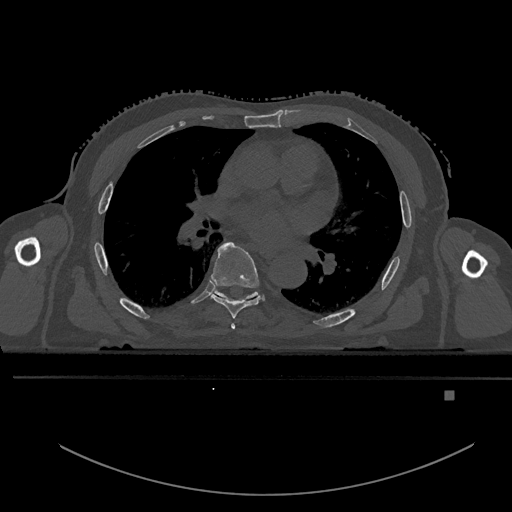
CT including the spine, one axial slice; position 296 of 969 along the scan axis; bone window (W 1800 / L 400 HU); 512 × 512 image matrix, field of view 456 × 456 mm. Male patient, age 82 years. From the clinical record (not read from this slice): primary cancer: prostate; vertebrae with lytic lesions (as recorded): T11, T9, T8, T2.
Structures marked on this image (semi-automatic segmentation, software-assisted and operator-edited):
- T5 vertebra: bounding box (x1, y1, x2, y2) in pixels: (231, 323, 236, 330)
- T6 vertebra: (211, 241, 260, 319)
- T7 vertebra: (214, 291, 256, 298)